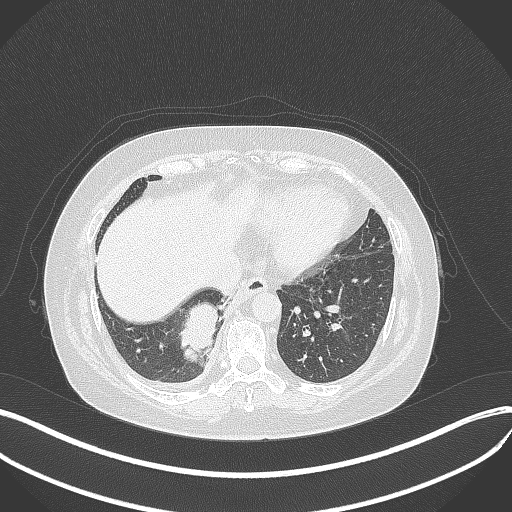
Chest CT, one axial slice; position 102 of 381 along the scan axis; lung window (W 1500 / L -600 HU); 512 × 512 image matrix, field of view 400 × 400 mm. Patient: female, 56 years. From the clinical record (not read from this slice): clinical TNM (as recorded): T2b N1 M0.
Outlined on this slice (rectangle marked by the reading radiologist):
- lung tumour (recorded histology: small cell carcinoma): bounding box <177,295,226,365> (left, top, right, bottom; pixels)